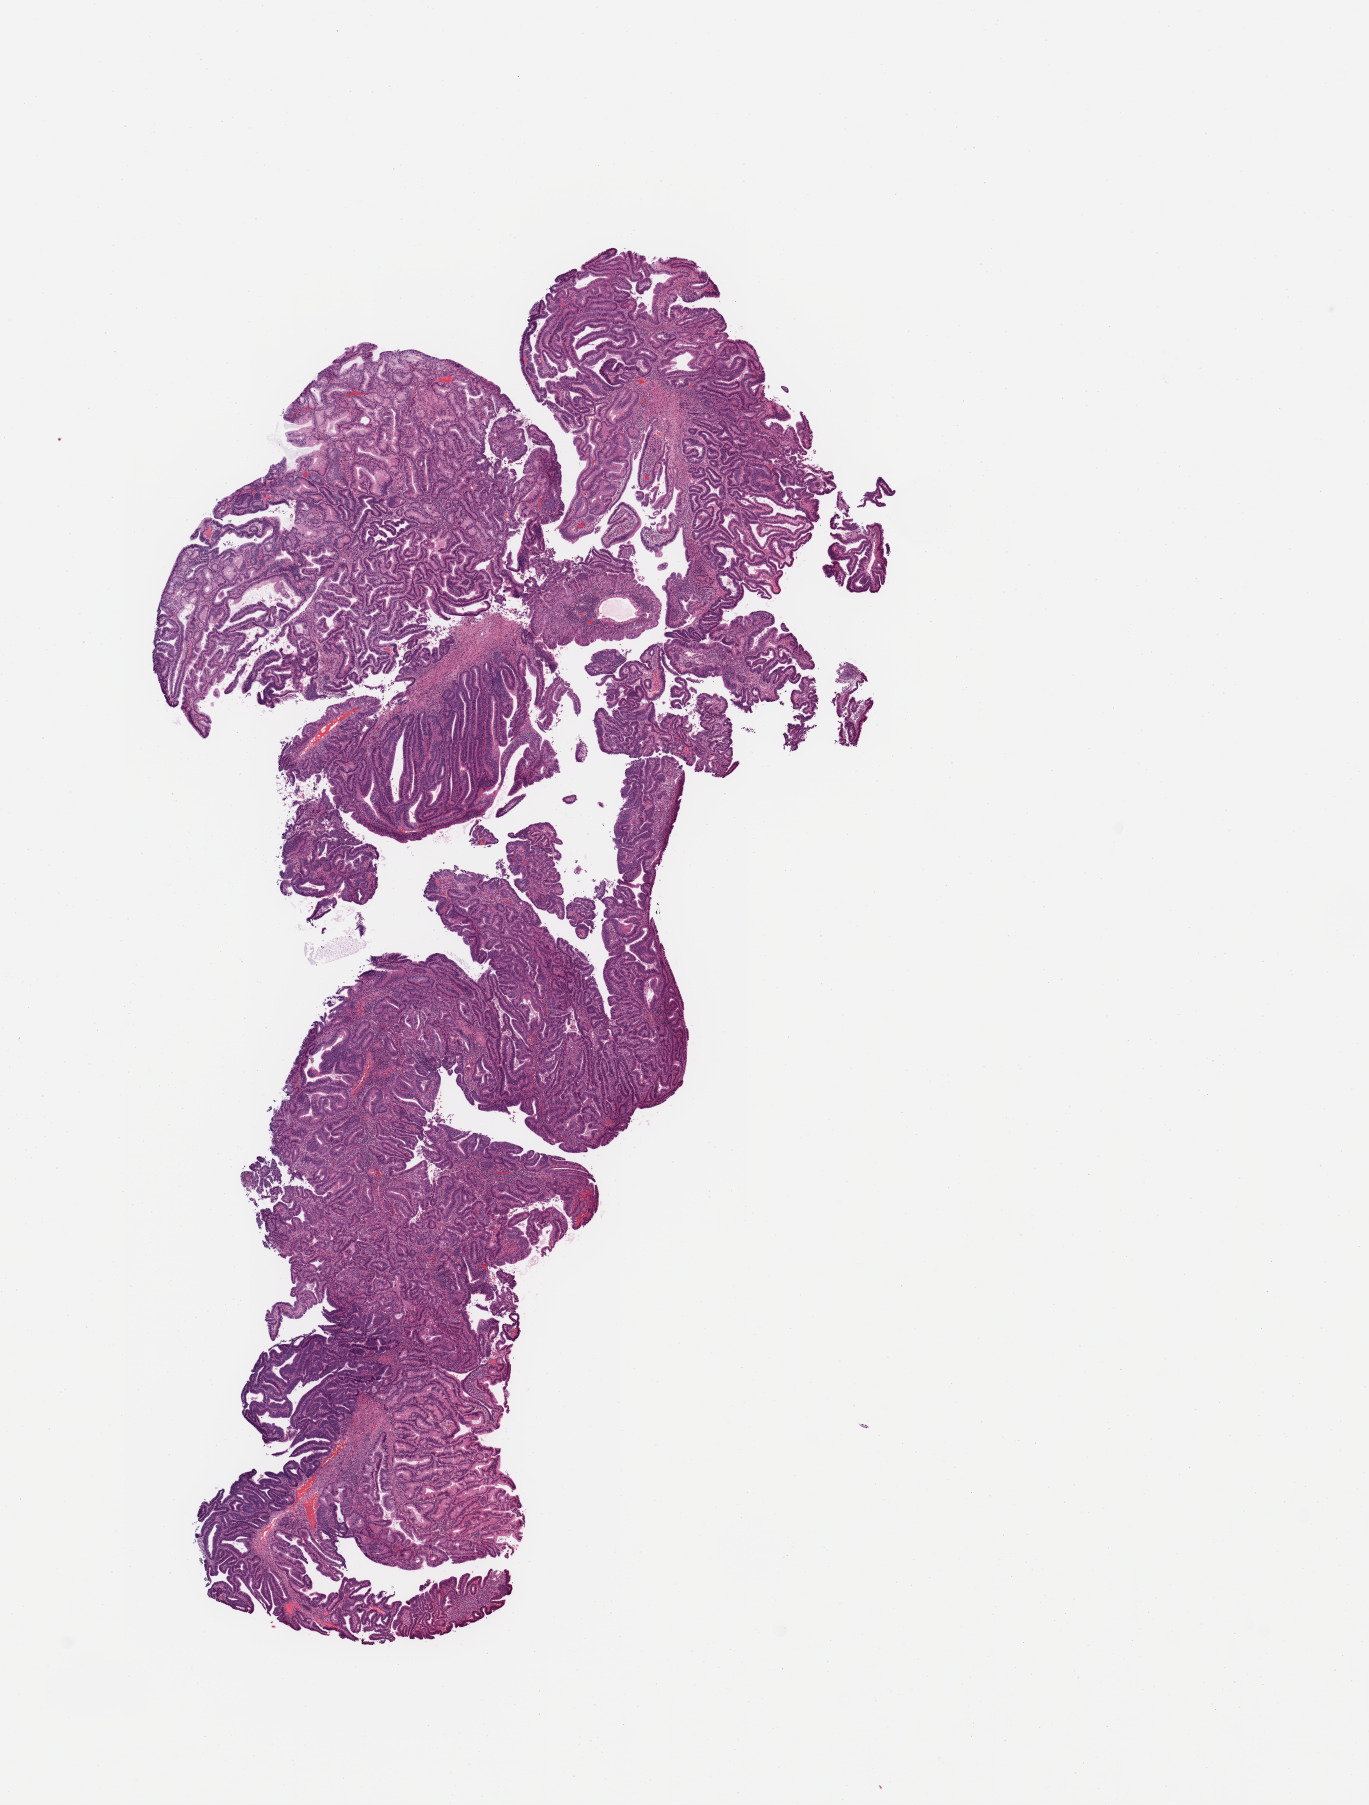
Digitized H&E tissue section (whole slide) — whole scanned area (about 10.8 x 14.3 mm) shown as a low-resolution overview. Tumour tissue sample, sampled site: uterus. 50-year-old female patient. Histologic grade: G1 (well differentiated). Composition of this section per pathologist review: tumour nuclei 95%, necrosis 0%.
AJCC pathologic stage: III. Histologic diagnosis: Endometrioid adenocarcinoma, NOS.